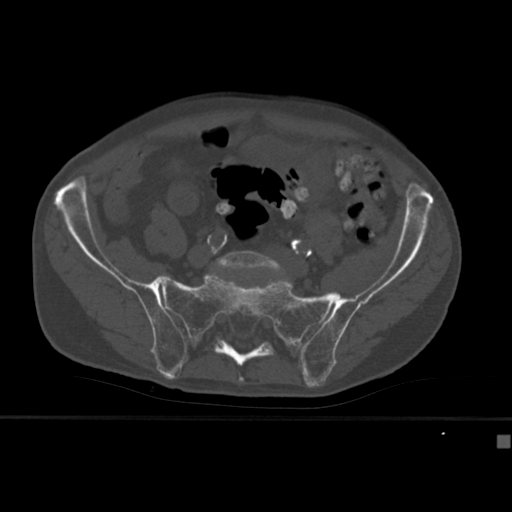
CT including the spine, one axial slice. Position 69 of 430 along the scan axis. 120 kVp. Bone window (W 1800 / L 400 HU). 1.5 mm slice thickness. 512 × 512 image matrix, field of view 337 × 337 mm. Male patient, age 64 years. From the clinical record (not read from this slice): primary cancer: uterus; vertebrae with lytic lesions (as recorded): T1, T4, T5, T7, L5.
Structures marked on this image (semi-automatically segmented with operator editing):
- L5 vertebra: box from (x=215, y=251) to (x=282, y=271) px